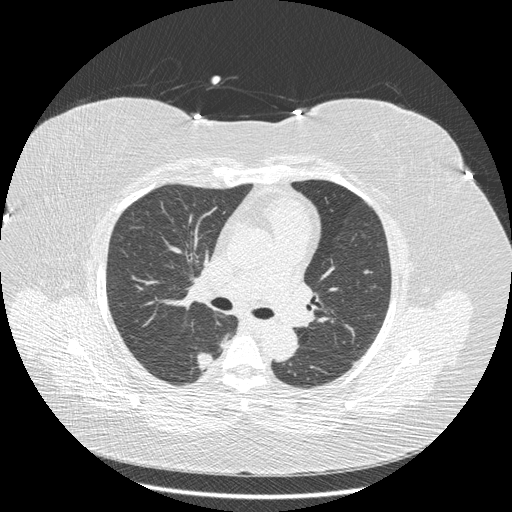
Low-dose screening chest CT, axial slice; first (baseline) screen; lung window (W 1500 / L -600 HU); 1.25 mm slice thickness; 120 kVp; slice 81 of 211 in the series. Female participant, aged 58 years at enrolment. Current smoker at enrolment.
Expert-annotated lung lesion, bounding box [x1, y1, x2, y2] px = [185, 344, 226, 382]. Screening reader's record for this exam (one nodule recorded; not confirmed to be the boxed lesion): non-calcified nodule or mass ≥4 mm, right lower lobe, 15 × 10 mm, smooth margins, soft tissue attenuation. Later outcome: lung cancer diagnosed 362 days after this screen — adenocarcinoma, NOS, right lower lobe, stage IB (AJCC 6th edition), 15 mm at pathology.